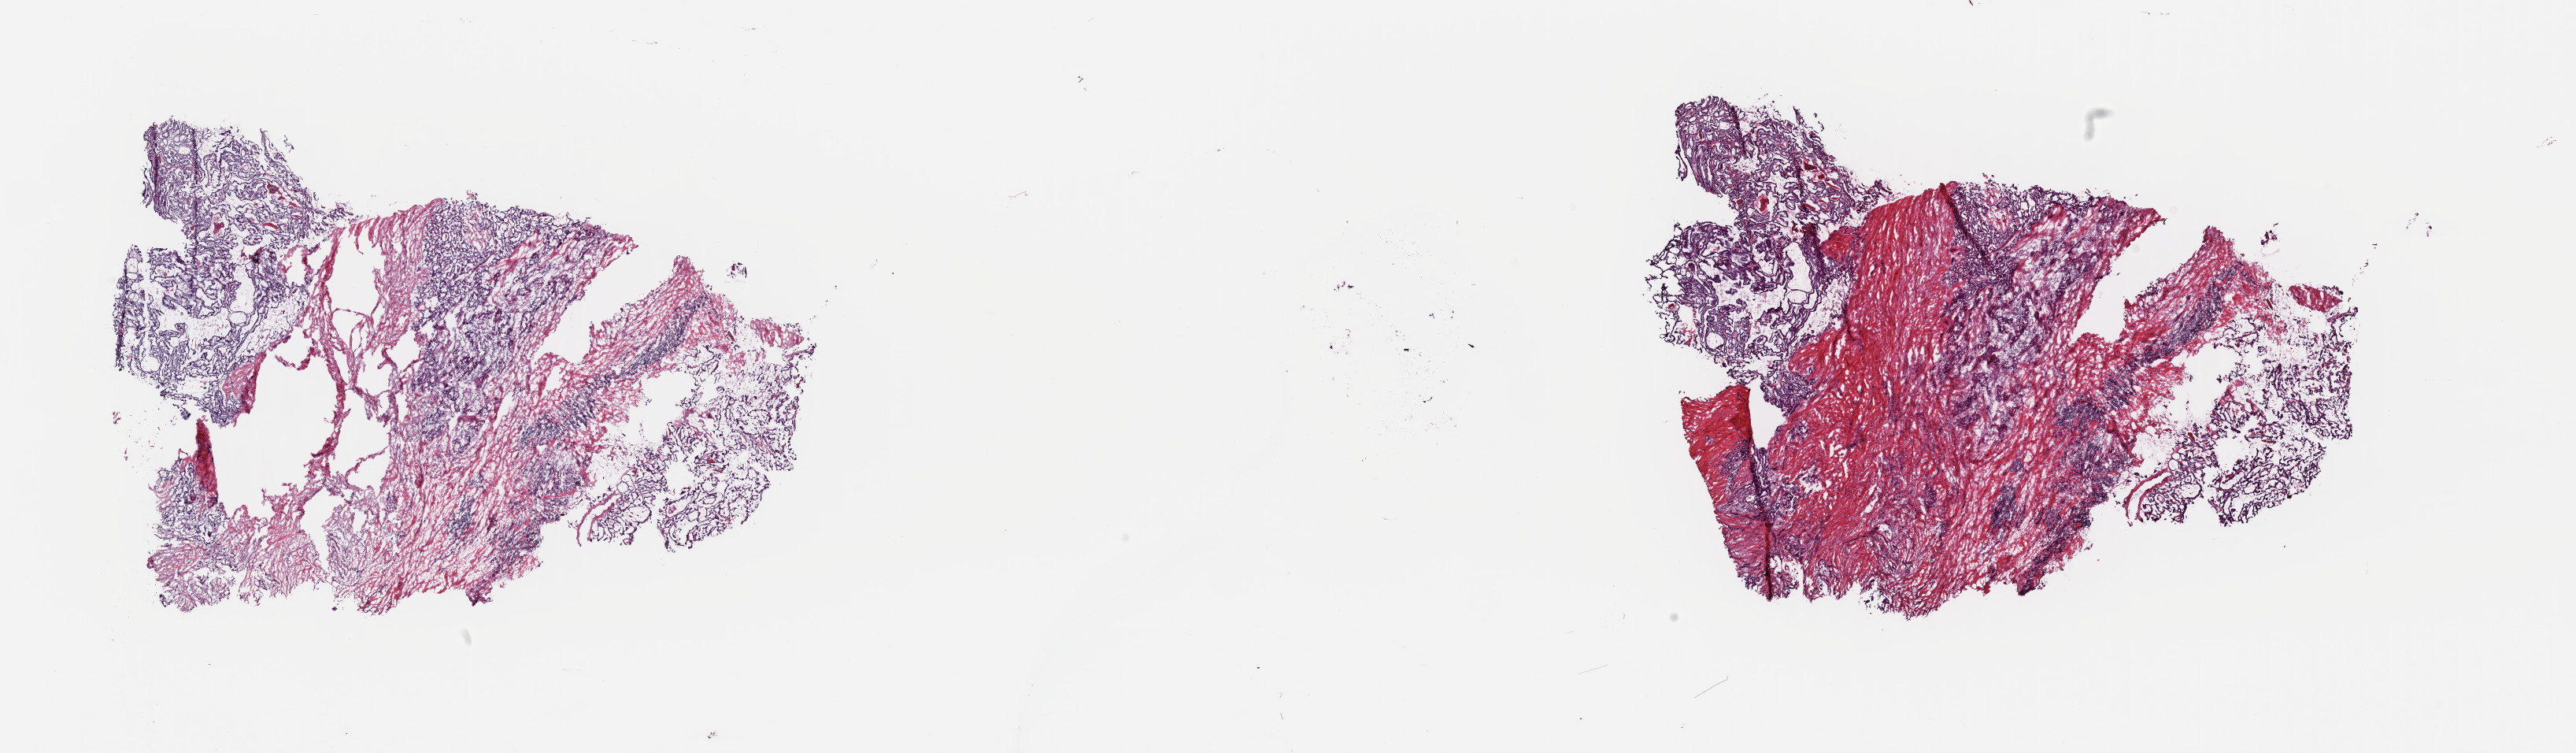
Digitized Hematoxylin and eosin (H&E) stained tissue section (whole slide), low-resolution overview of the scanned area, about 25.8 x 7.6 mm (acquisition: 40x scan), frozen section, thyroid, primary tumour sample. Male, age 40 years at initial diagnosis. Composition of this section per pathologist review: tumour cells 70%, tumour nuclei 70%, normal cells 0%, stromal cells 30%, necrosis 0%. Inflammatory infiltration, as recorded: lymphocyte infiltration 10%, monocyte infiltration 0%, neutrophil infiltration 0%.
Histologic diagnosis: Papillary adenocarcinoma, NOS (thyroid gland). AJCC pathologic stage: I (6th edition). Laterality: bilateral. Lymph nodes positive (case pathology): 9 of 38 examined.